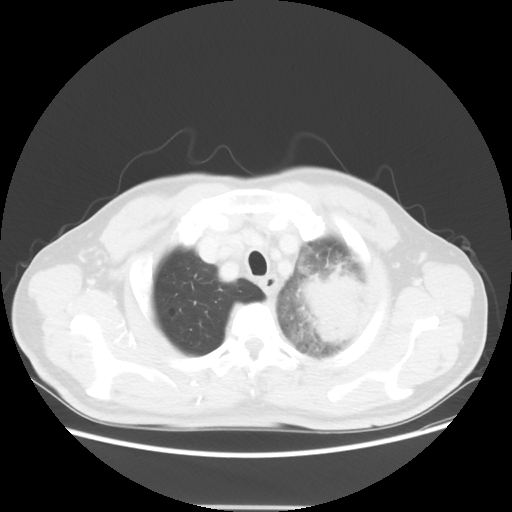
Chest CT, one axial slice; position 49 of 53 along the scan axis; lung window (W 1500 / L -600 HU); 512 × 512 image matrix, field of view 391 × 391 mm. Male patient, age 60 years. From the clinical record (not read from this slice): clinical TNM (as recorded): T4 N1 M1a; histopathological grade: G3.
Annotated regions visible in this slice (bounding box drawn by a radiologist):
- lung tumour (recorded histology: large cell carcinoma): bounding box <298,266,381,342> (left, top, right, bottom; pixels)